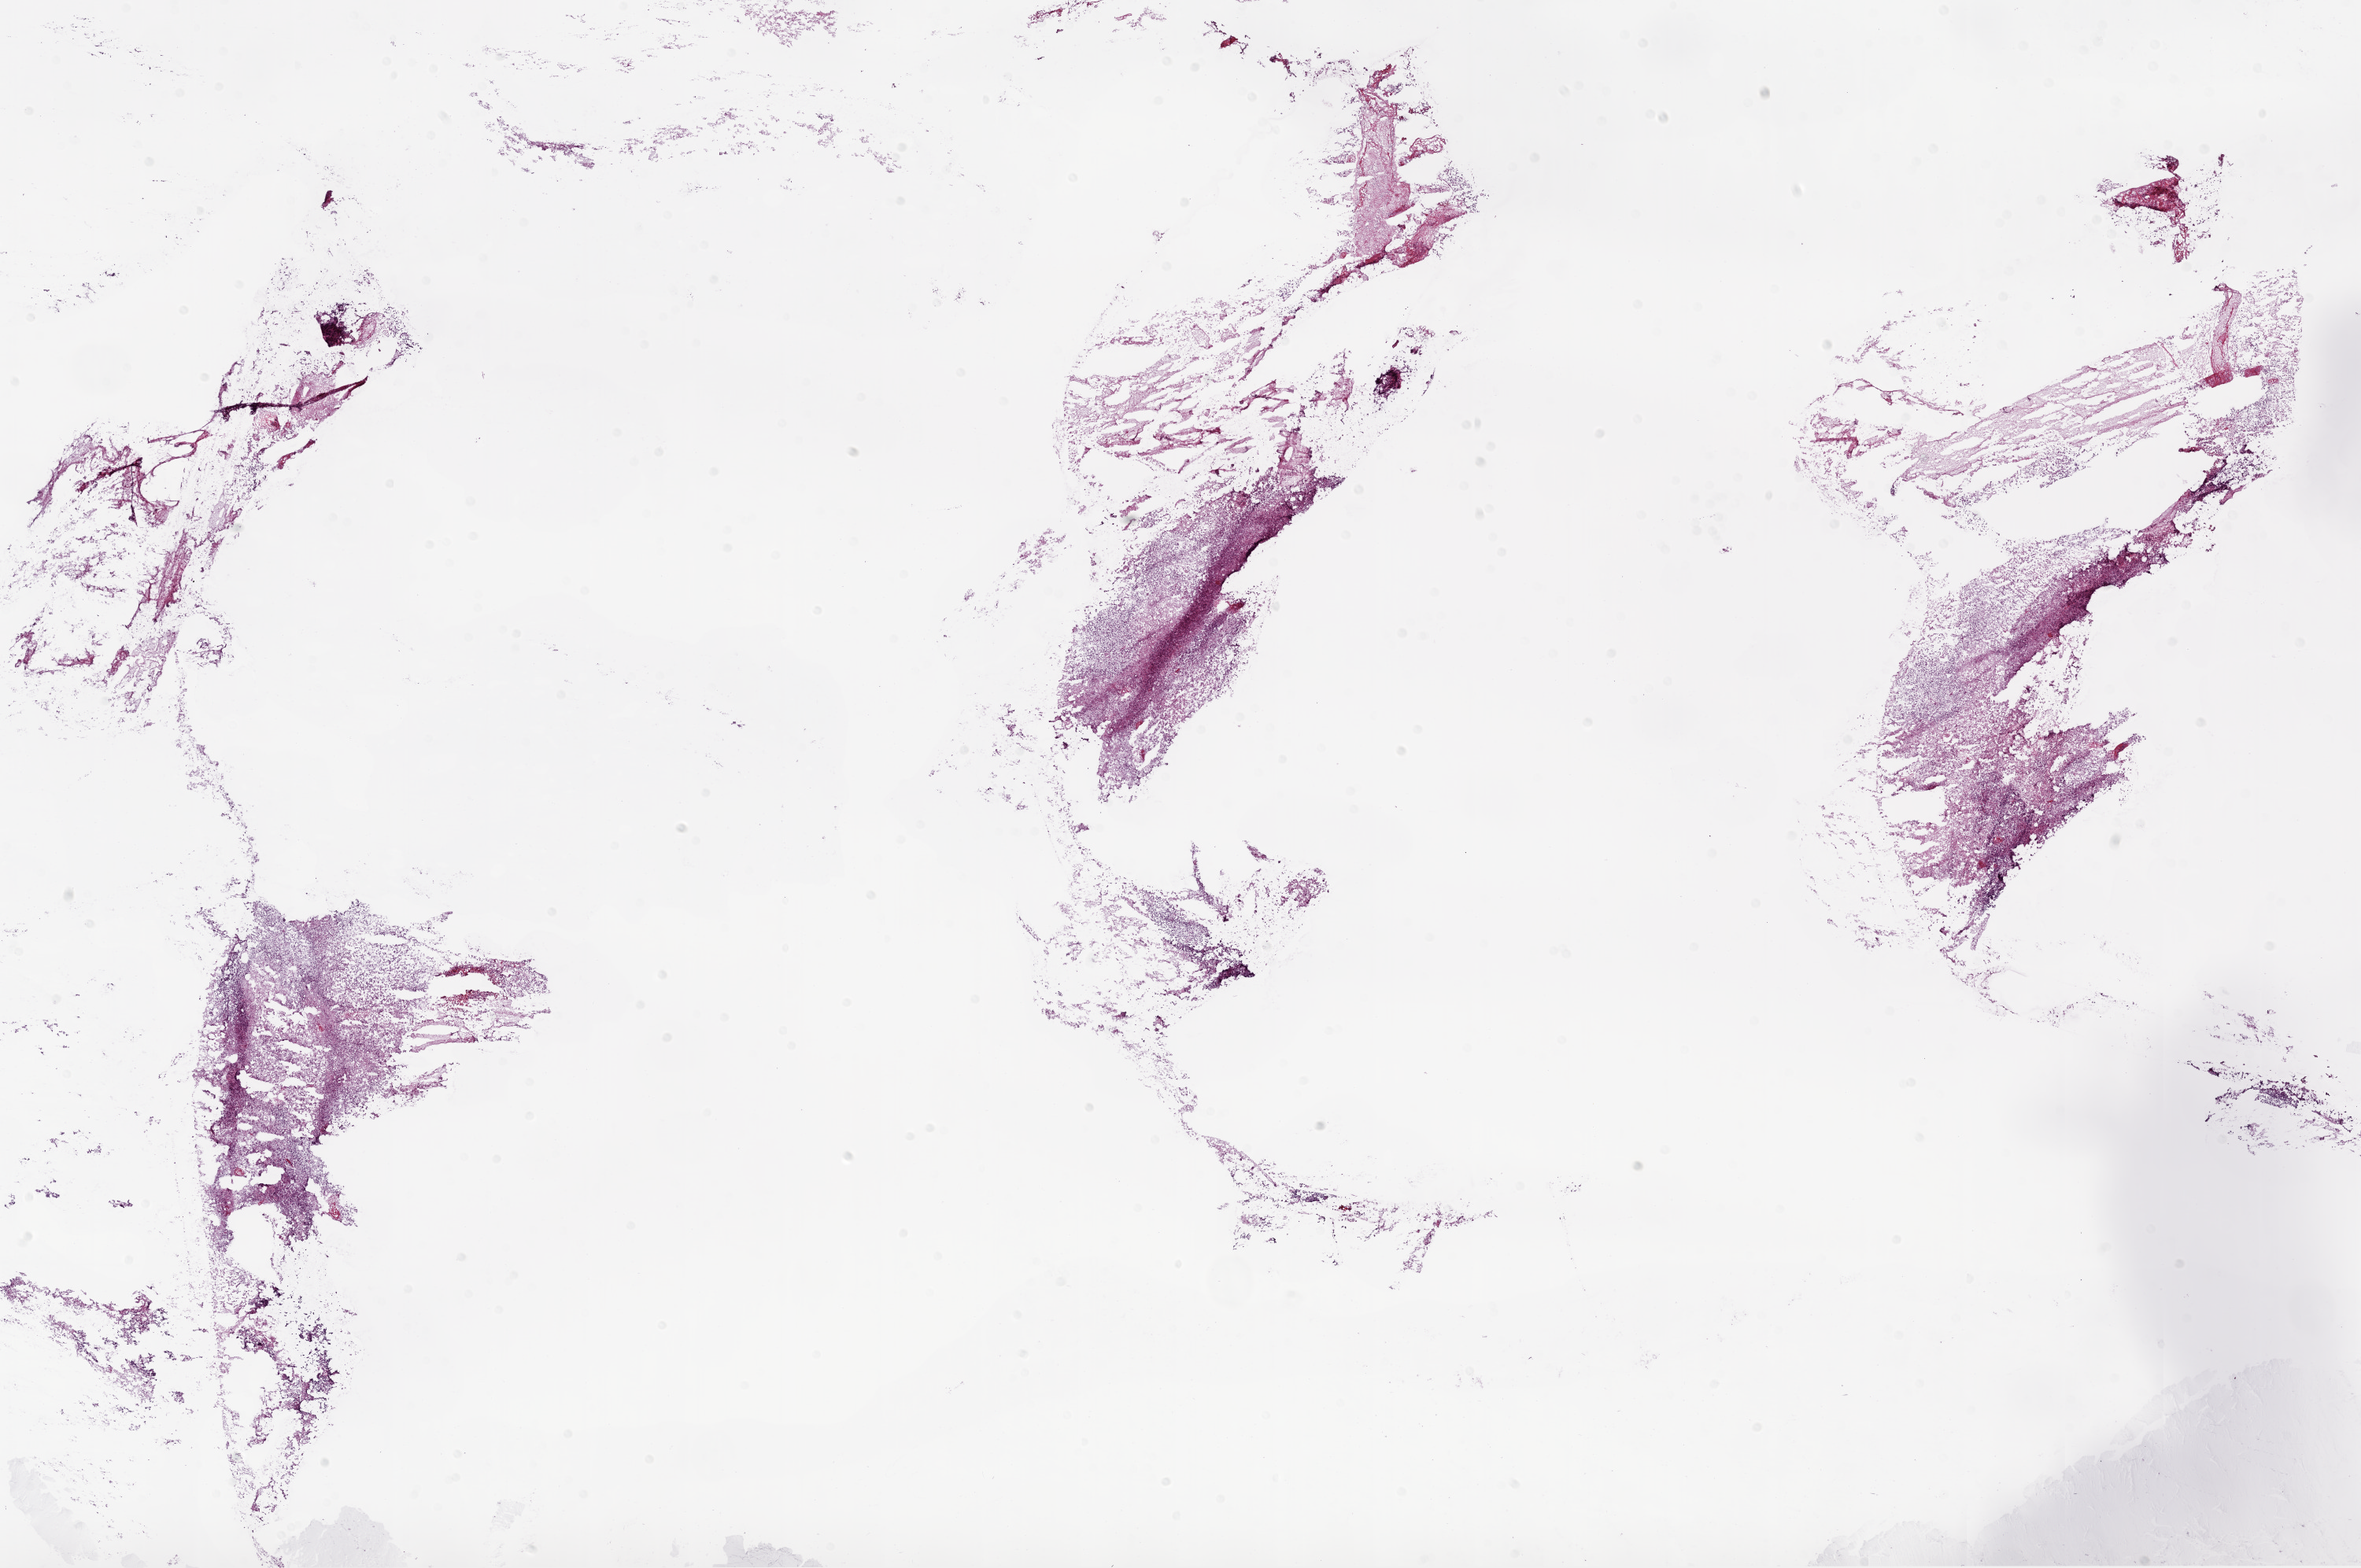
Digitized Hematoxylin and eosin (H&E) stained tissue section (whole slide), shown as a low-resolution overview of the whole scanned area (about 24.1 x 16.0 mm). Frozen section from the bottom of the tissue portion. Primary tumour sample from the brain. Patient: male, age at initial diagnosis 67 years. Pathologist review of this section (percent, as recorded): tumour cells 90%, tumour nuclei 100%, normal cells 0%, stromal cells 0%, necrosis 10%.
• diagnosis: Glioblastoma